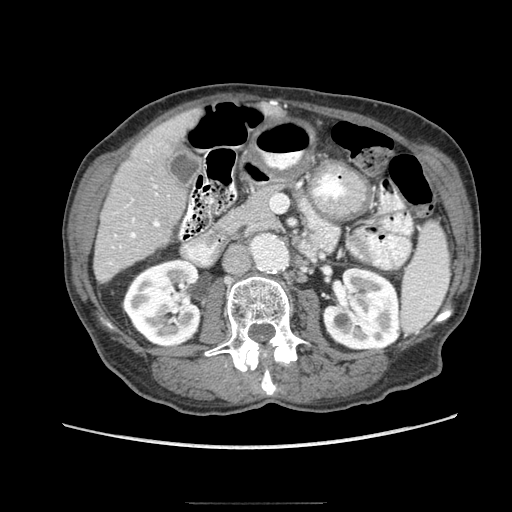
Contrast-enhanced abdominal CT (liver protocol), one axial slice; slice 30 of 83 in the series (ordered by position); 140 kVp; soft-tissue window (W 400 / L 40 HU); 2.5 mm slice thickness; 512 × 512 image matrix, field of view 360 × 360 mm. From the clinical record (not read from this slice): diagnosis: hepatocellular carcinoma (patient treated with transarterial chemoembolisation; whether this scan precedes or follows treatment is not stated here); TNM stage (as recorded): Stage-I; Child-Pugh class: A; tumour differentiation: moderately differentiated.
Structures marked on this image (semi-automatic segmentation, software-assisted and operator-edited):
- liver parenchyma outside the tumour (the mass and vessels are separate outlines, so this box may not span the whole liver): box from (x=94, y=108) to (x=202, y=282) px
- liver vessels: (x=109, y=151)–(x=160, y=265)